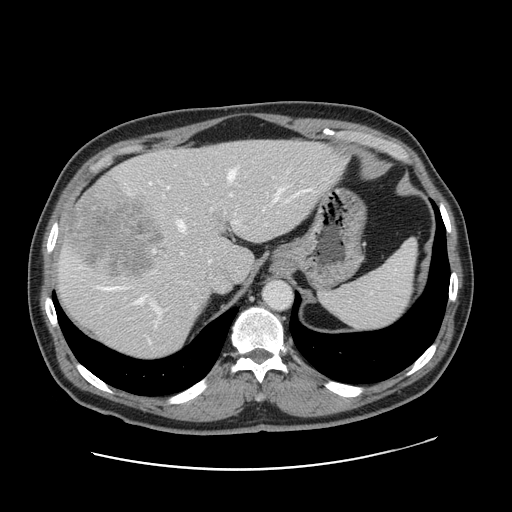
Contrast-enhanced abdominal CT, one axial slice; slice 121 of 178 in the series (ordered by position); 120 kVp; intravenous contrast given; soft-tissue window (W 400 / L 40 HU); 2.5 mm slice thickness; 512 × 512 image matrix. Male patient, age 63 years. From the clinical record (not read from this slice): diagnosis: colorectal cancer liver metastases, imaged before liver resection; multiple liver metastases: yes; largest metastasis: 8 cm; disease in both lobes: yes.
Outlined on this slice (manually delineated by an expert):
- hepatic veins: bounding box (x1, y1, x2, y2) in pixels: (98, 170, 281, 303)
- liver: (57, 140, 344, 359)
- planned liver remnant (the part of the liver to remain after resection): (143, 141, 344, 280)
- portal vein (with intrahepatic branches): (153, 186, 240, 325)
- liver metastasis: (64, 196, 163, 278)